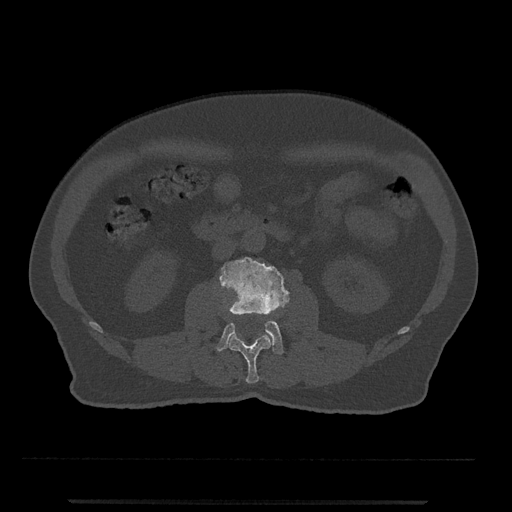
CT including the spine, one axial slice. Bone window (W 1800 / L 400 HU). 0.5 mm slice thickness. 512 × 512 image matrix, field of view 419 × 419 mm. Patient: male, 63 years. From the clinical record (not read from this slice): primary cancer: prostate.
Outlined on this slice (semi-automatic segmentation, software-assisted and operator-edited):
- L2 vertebra: bounding box (x1, y1, x2, y2) in pixels: (228, 333, 271, 383)
- L3 vertebra: (216, 256, 290, 354)